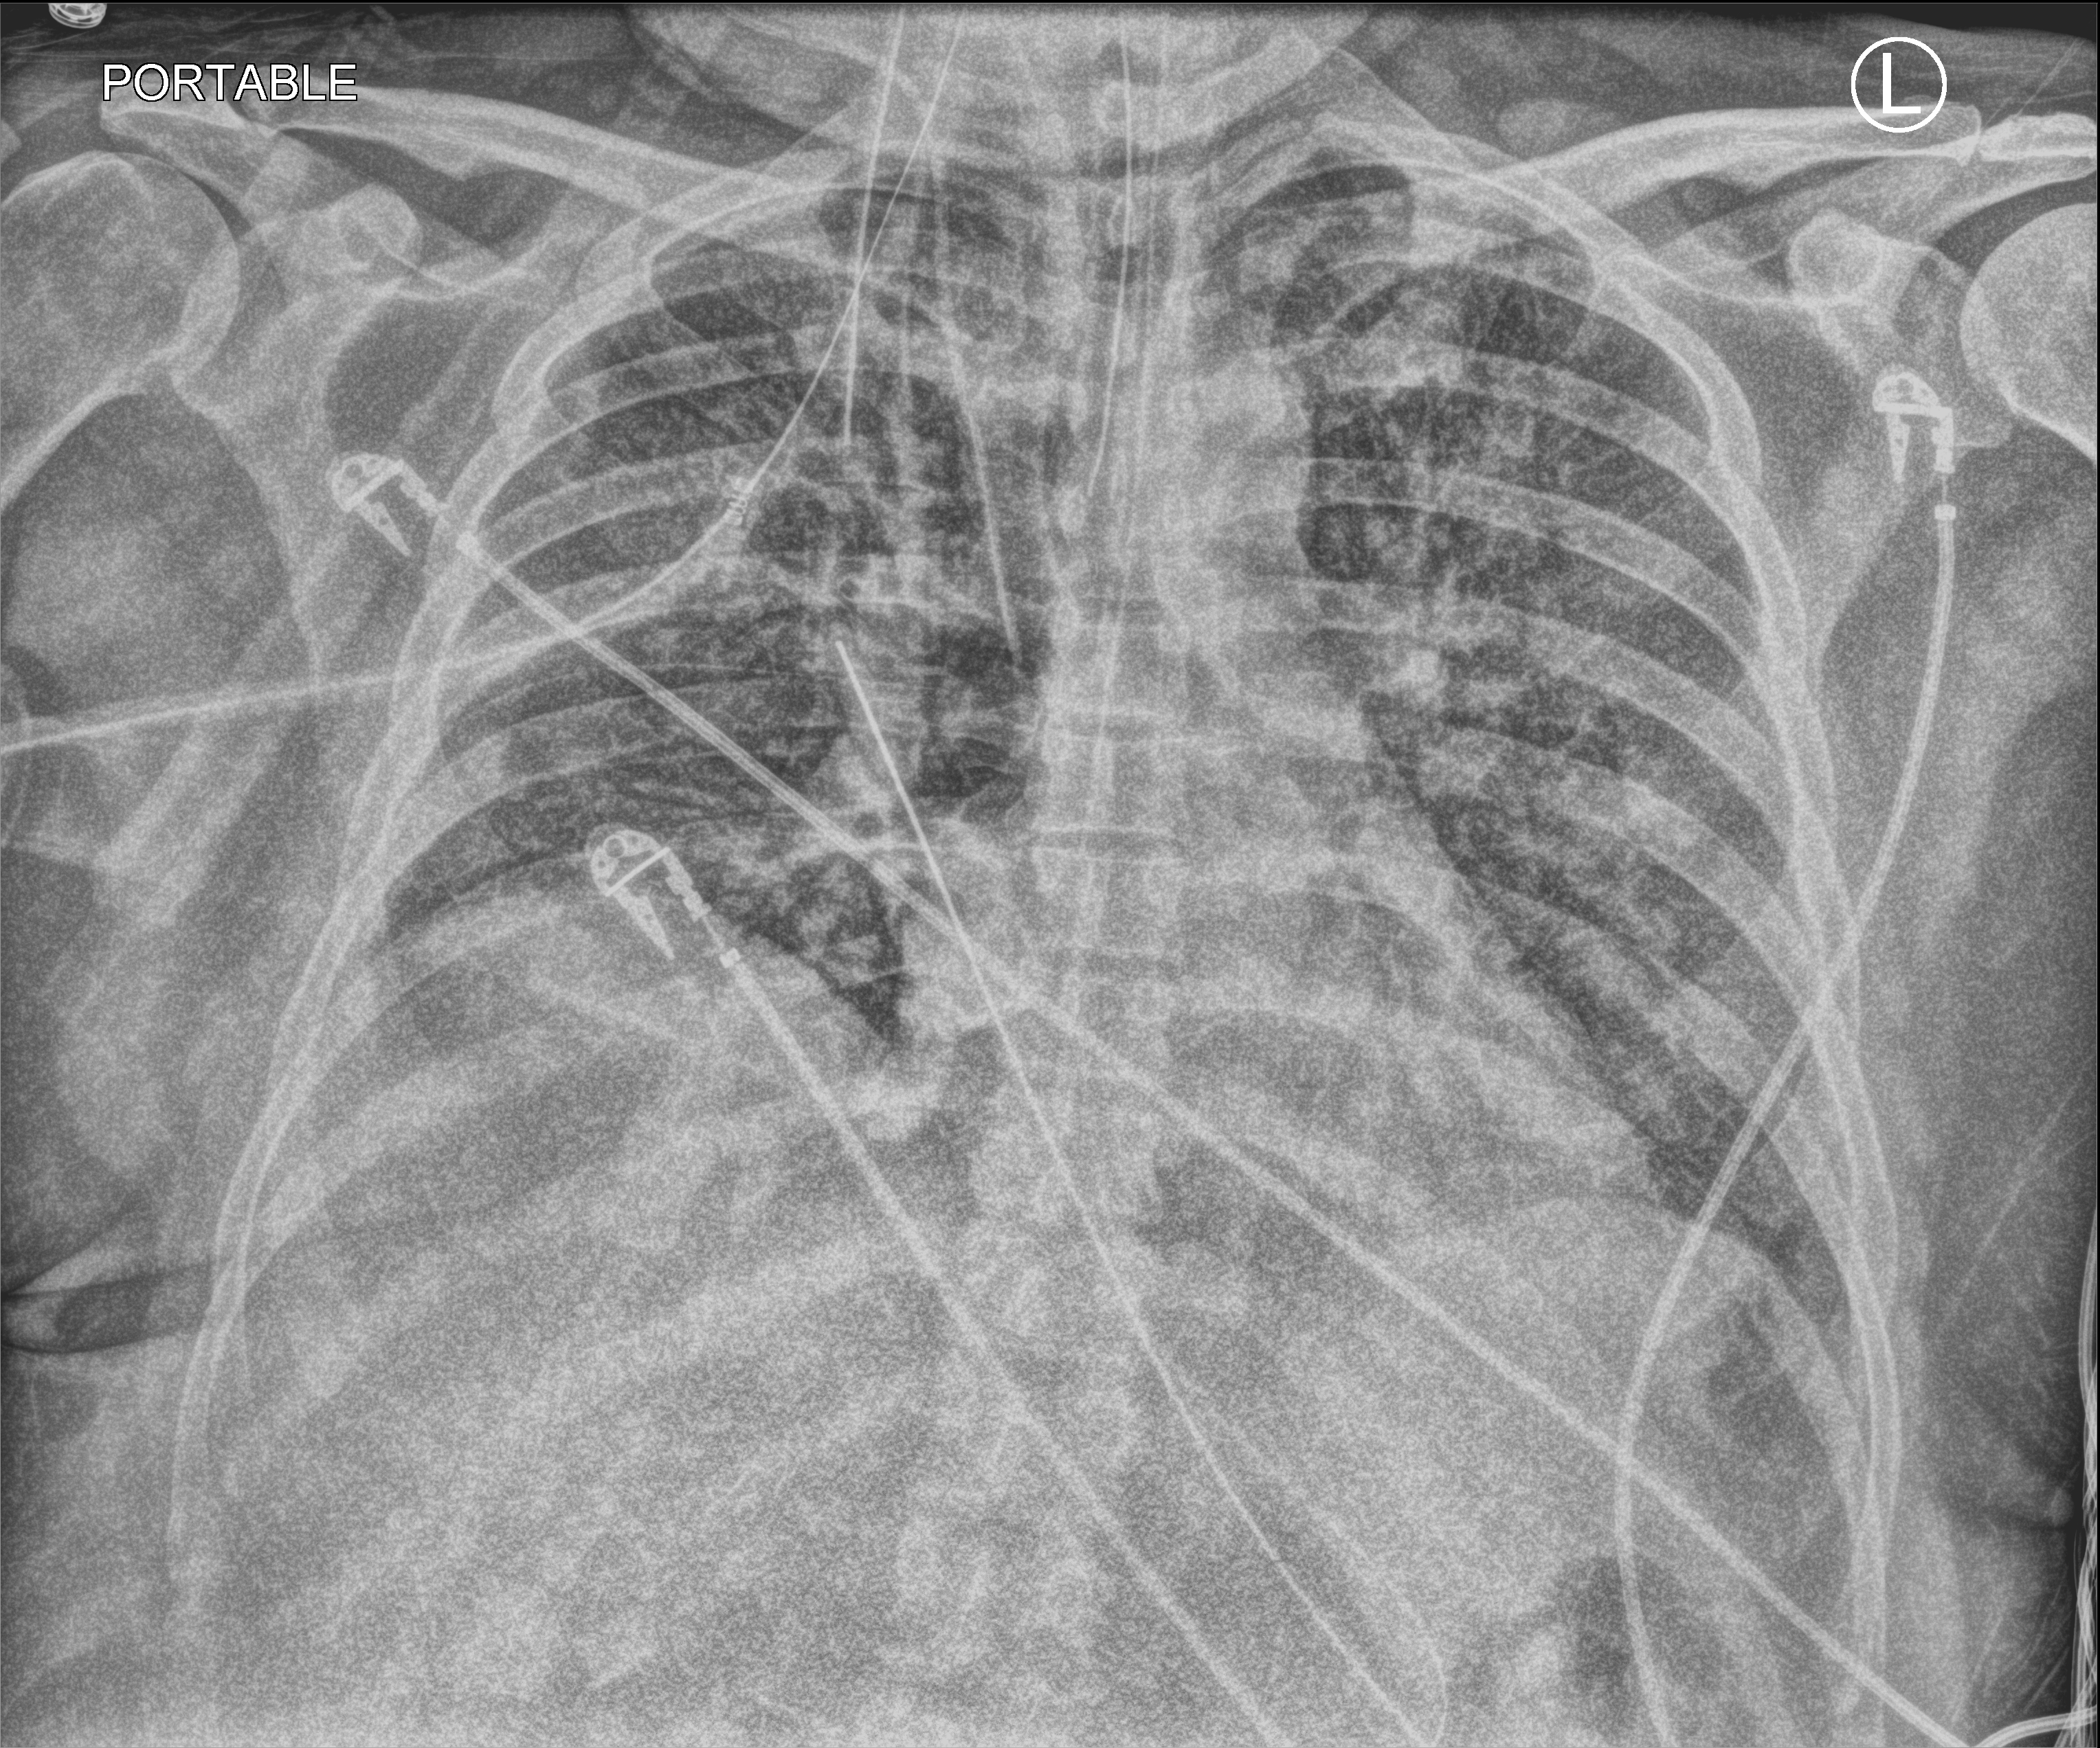
Bedside chest radiograph (computed radiography); anteroposterior (AP) projection. Male patient hospitalised with COVID-19, age 18–59 years.
Admission-level facts for this patient (not findings on this image; timing relative to this image not recorded):
- chronic kidney disease (admission record): no
- length of hospital stay: 96 days
- mechanically ventilated during this hospital stay: yes